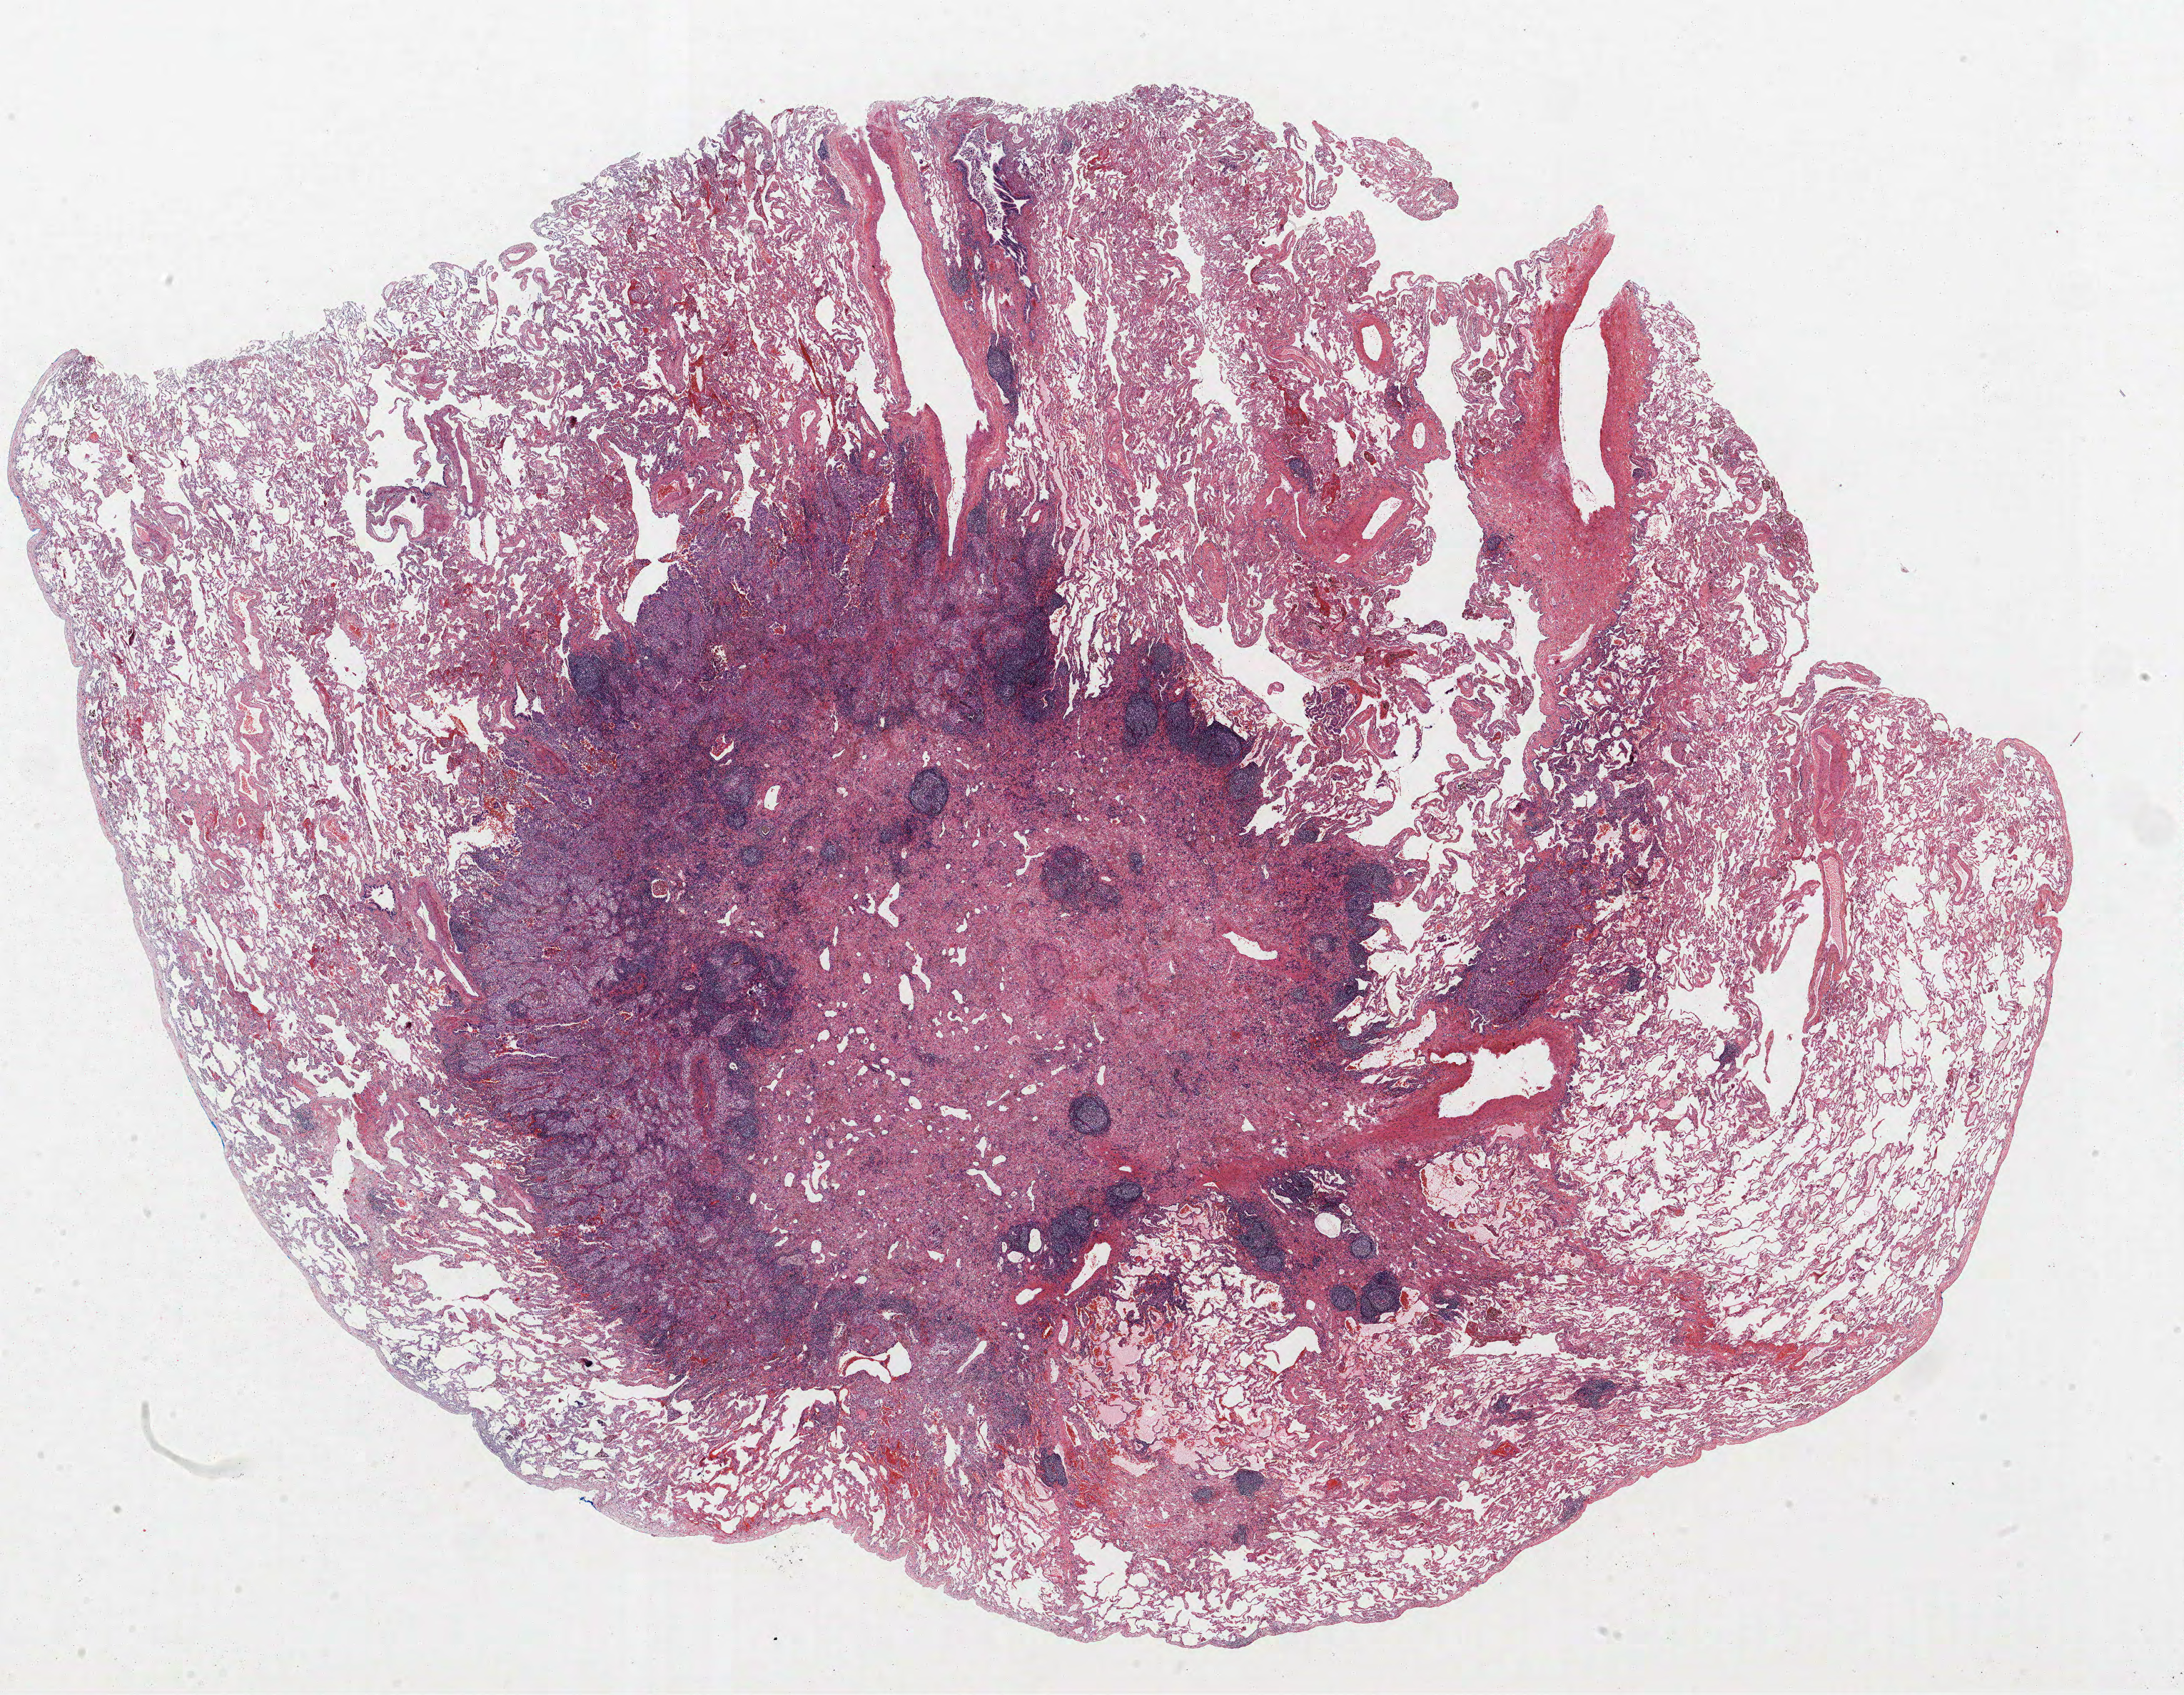
Whole-slide histology image, Hematoxylin and eosin (H&E) stained — a low-resolution overview of the entire scanned area, about 24.5 x 19.0 mm (acquisition: 40x scan), FFPE section, lung tissue. Female patient, aged 65 at enrolment. Current smoker at enrolment. Grade: moderately differentiated (G2).
Primary tumour location (clinical record): right upper lobe. Stage (AJCC 6th edition): IA. Participant's lung-cancer diagnosis: Acinar cell carcinoma. Tumour size (pathology): 15 mm.